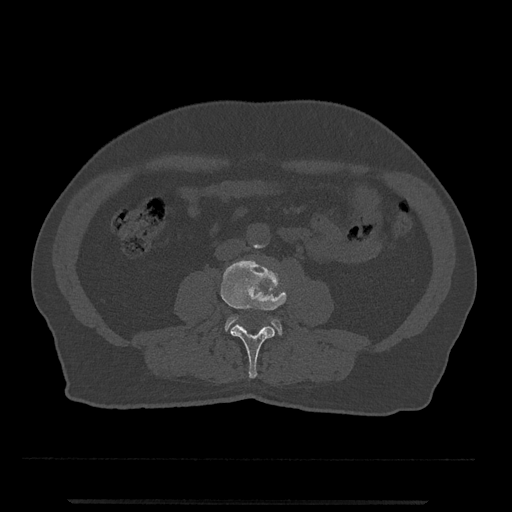
CT including the spine, one axial slice; slice 183 of 797 in the series (ordered by position); bone window (W 1800 / L 400 HU); 0.5 mm slice thickness; 512 × 512 image matrix, field of view 419 × 419 mm. Patient: male, 63 years. From the clinical record (not read from this slice): primary cancer: prostate.
Annotated regions visible in this slice (semi-automatically segmented with operator editing):
- L3 vertebra: bounding box [x1, y1, x2, y2] px = [220, 259, 287, 379]
- L4 vertebra: [225, 317, 283, 335]